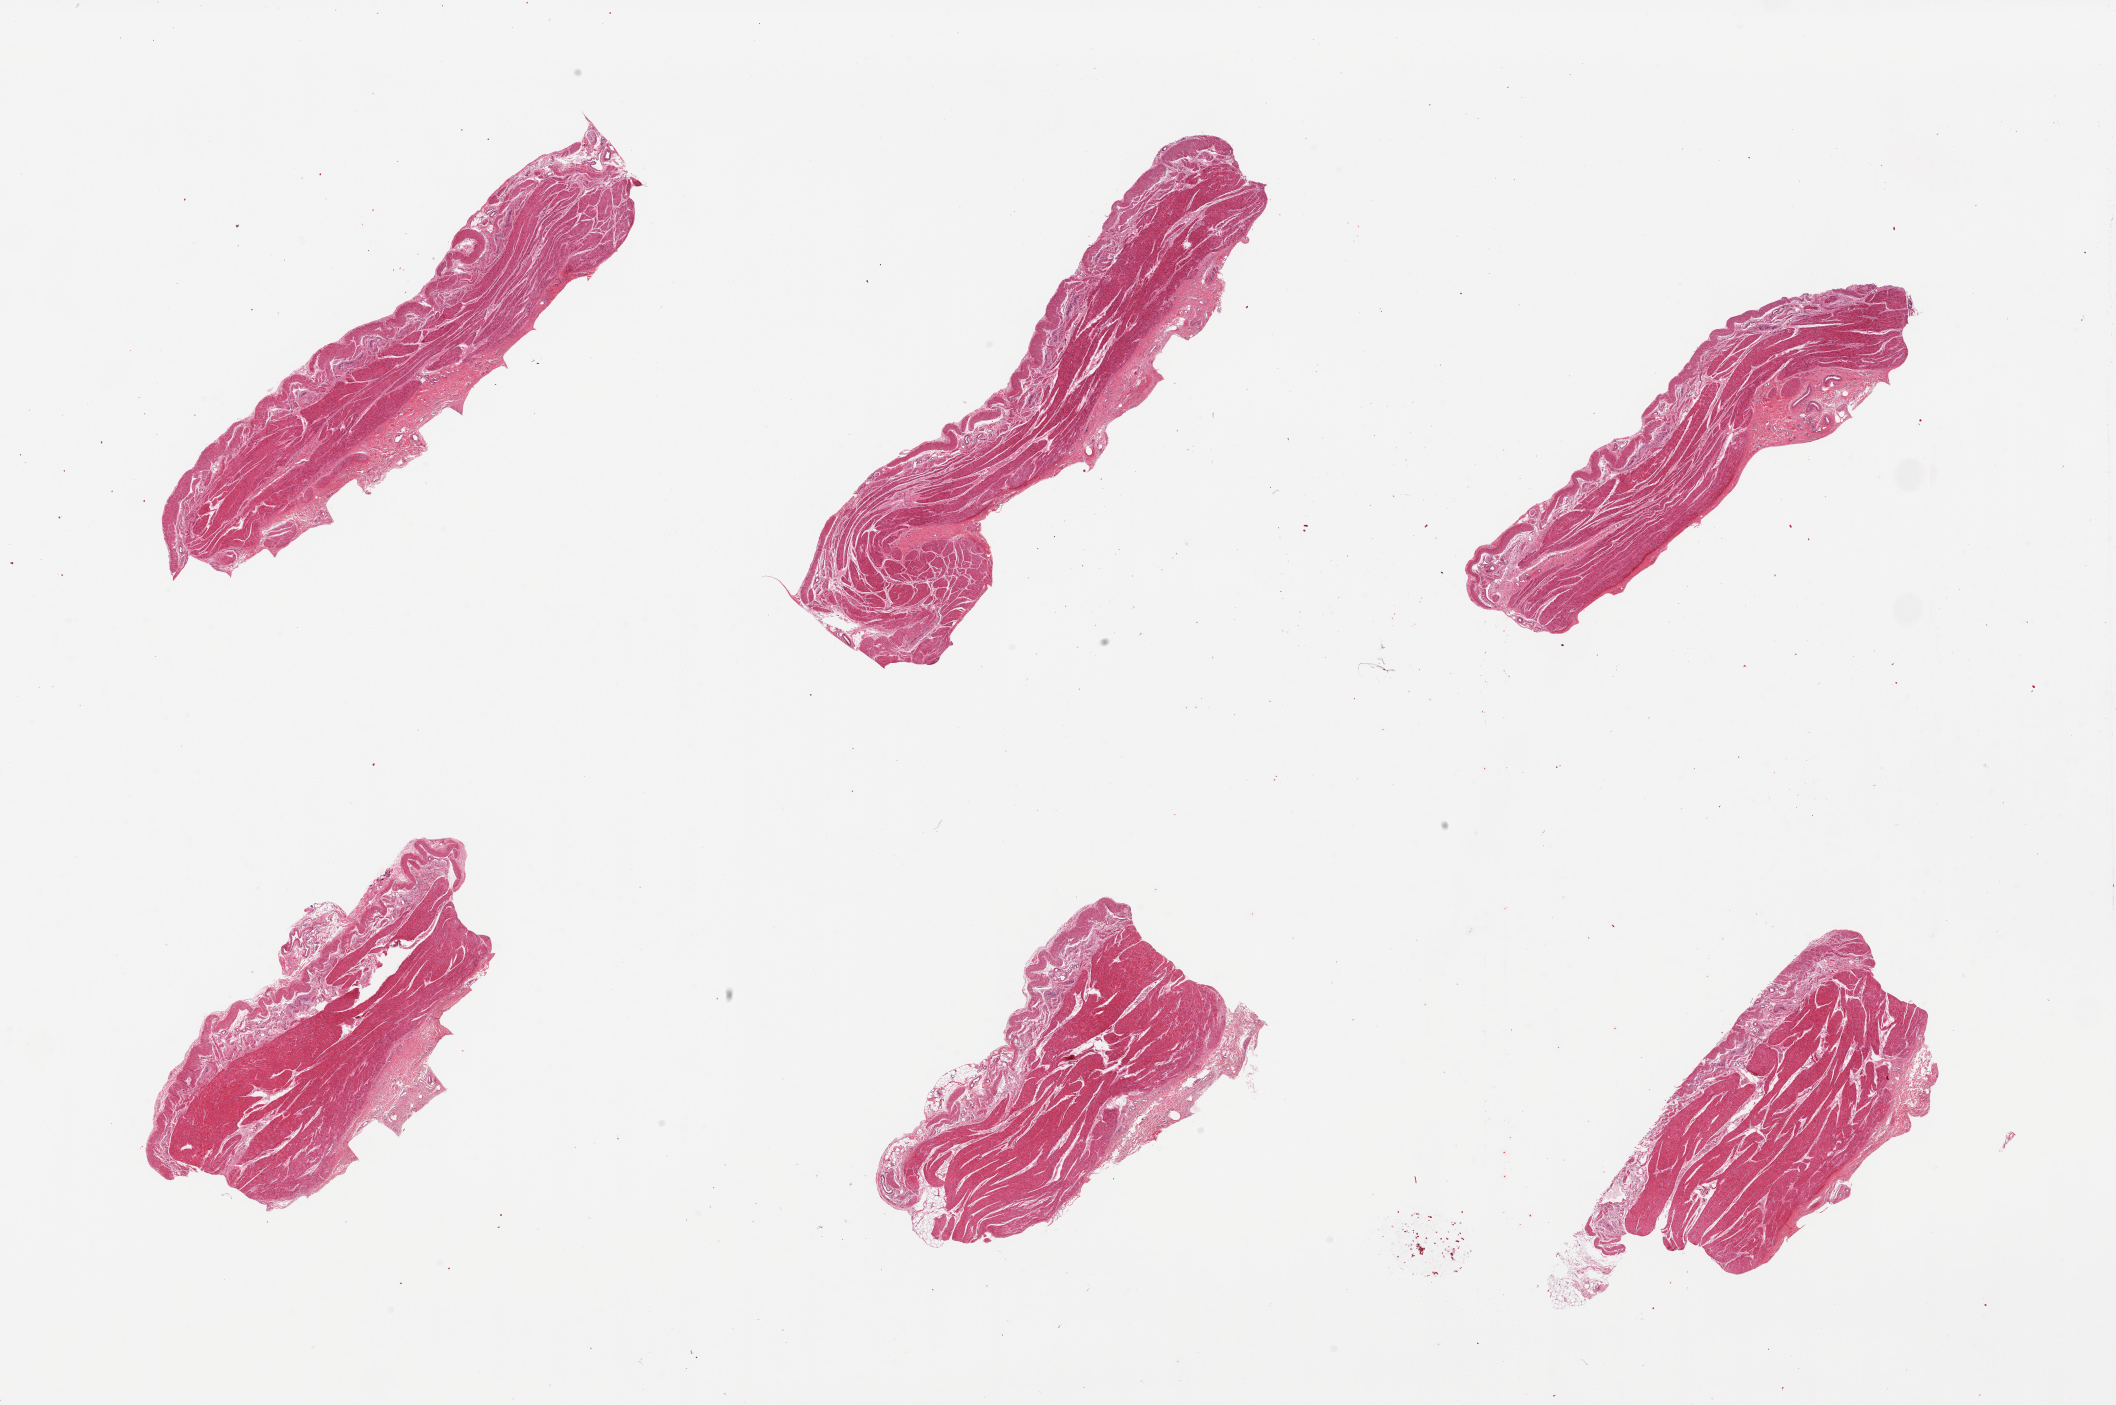
H&E whole-slide image, shown as a low-resolution overview of the whole scanned area (about 33.5 x 22.2 mm); PAXgene-fixed, paraffin-embedded tissue; section of gastroesophageal junction (target tissue); tissue donor sample. Donor sex: male.
Pathologist's review note for this sample: 6 pieces. Well dissected.